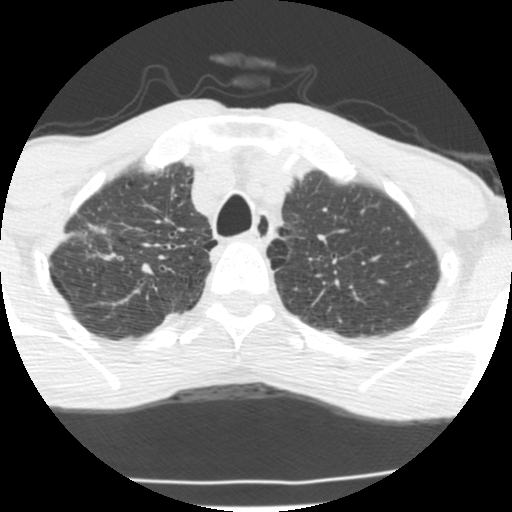
Chest CT (low-dose screening protocol), one axial image; second annual screen; lung window (W 1500 / L -600 HU); 2.5 mm slice thickness. Male participant, aged 62 years at enrolment.
• Lesion marked by an expert reader, box from (x=47, y=215) to (x=128, y=271) px.
• The exam's reader record, not a measurement of the box and not confirmed to be the same lesion: non-calcified nodule or mass ≥4 mm, right upper lobe, 23 × 11 mm, spiculated (stellate) margins, soft tissue attenuation, pre-existing on the prior screen: yes.
• Official screen result: positive, change unspecified: nodule(s) >= 4 mm or enlarging nodule(s), mass(es), or other non-specific abnormalities suspicious for lung cancer.
• Later outcome: lung cancer diagnosed 277 days after this screen — adenocarcinoma, NOS, right upper lobe, poorly differentiated (G3), stage IIA (AJCC 6th edition), 22 mm at pathology.